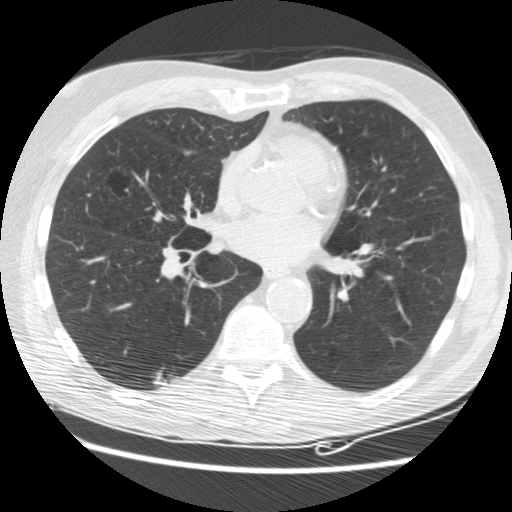
Chest CT (low-dose screening protocol), one axial image, third annual screen, lung window (W 1500 / L -600 HU), 2.5 mm slice thickness, standard (soft-tissue) reconstruction kernel (STANDARD). Male, age 62 years at enrolment. Current smoker at enrolment.
• Lesion marked by an expert reader, bounding box [x1, y1, x2, y2] px = [143, 363, 176, 395].
• The screening reader recorded 3 non-calcified nodules or masses ≥4 mm on this exam; which of them this box marks is not recorded.